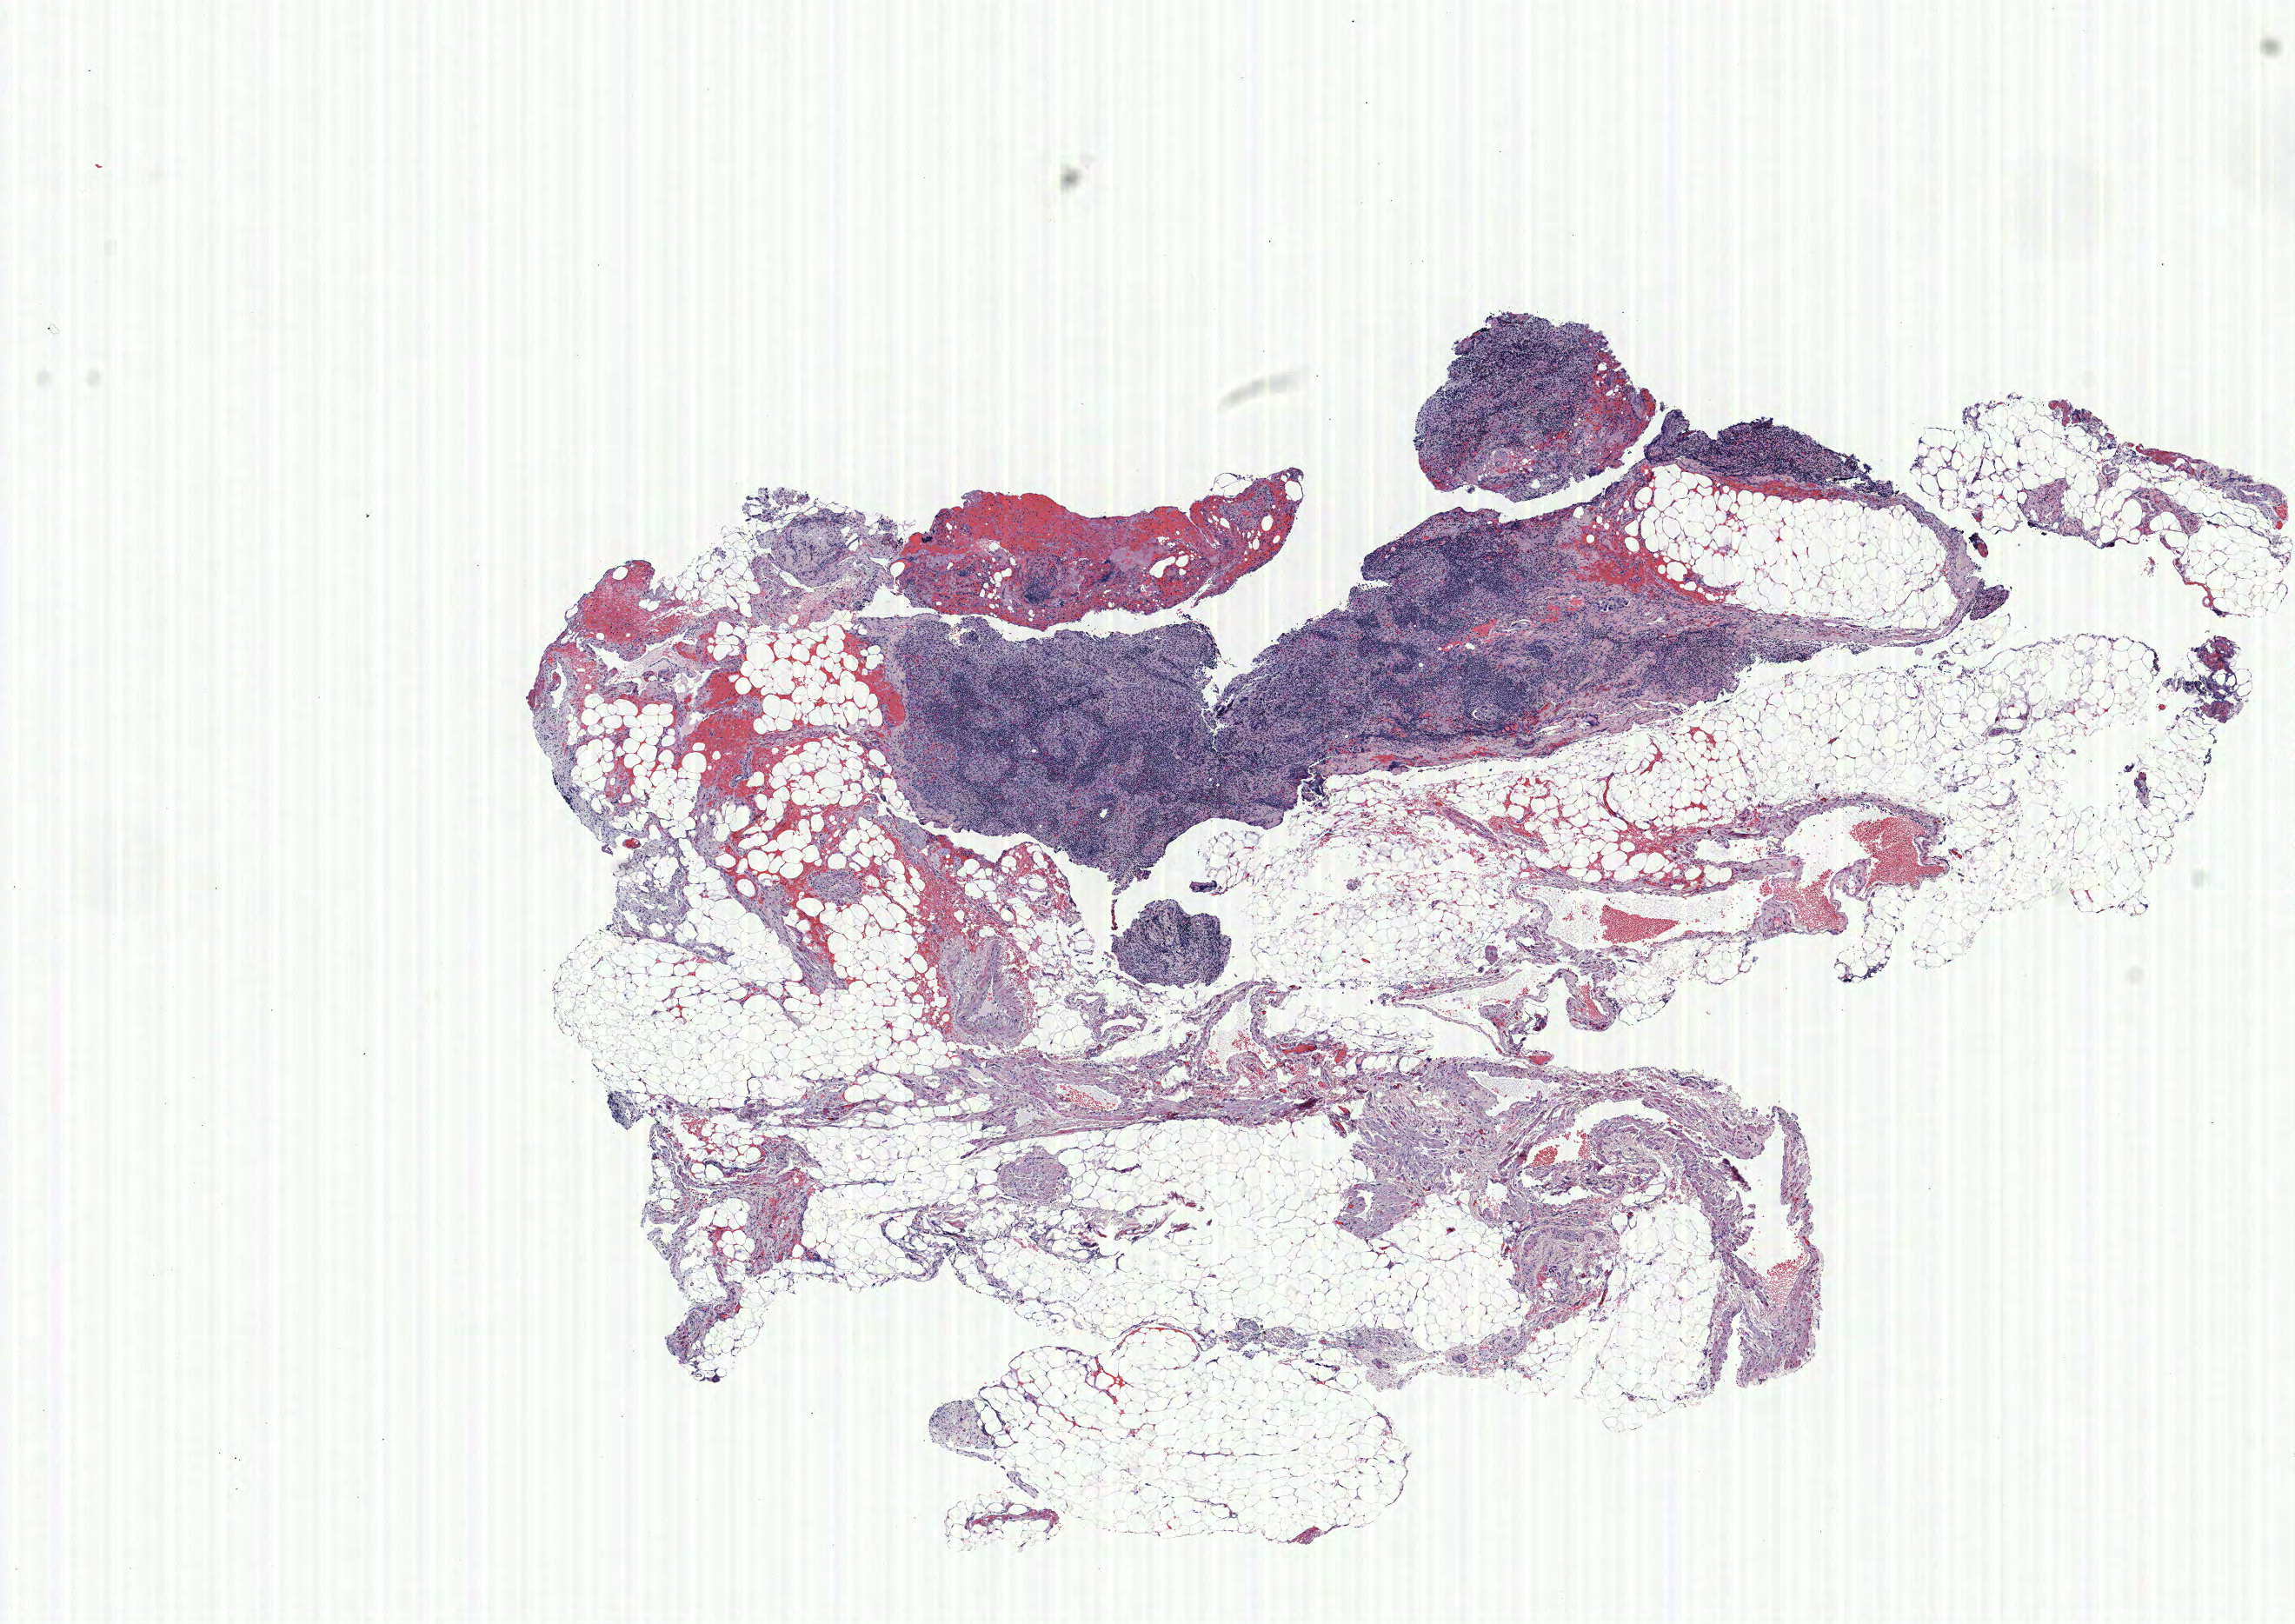
H&E-stained whole-slide image, shown as a low-resolution overview of the whole scanned area (about 10.6 x 7.5 mm). Formalin-fixed paraffin-embedded (FFPE) section. Lung tissue. Male, age 63 at enrolment. Grade: moderately differentiated (G2).
- tumour size (pathology): 45 mm
- primary tumour location (clinical record): right lower lobe
- participant's lung-cancer diagnosis: Adenocarcinoma, NOS
- ICD-O-3 topography: lower lobe of lung (C34.3)
- stage (AJCC 6th edition): IIIA